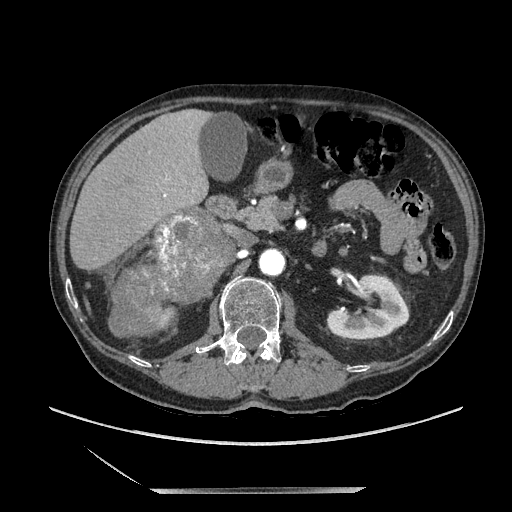
Contrast-enhanced abdominal CT, one axial slice. Soft-tissue window (W 400 / L 40 HU). 1.25 mm slice thickness. 512 × 512 image matrix, field of view 420 × 420 mm. Male patient. Case-level facts recorded for this patient, not image findings: diagnosis: adrenocortical carcinoma; tumour side: right adrenal; tumour size at pathology: 16 cm; Ki-67 index: 17 %; stage (as recorded): 3.
Outlined on this slice (semi-automatic segmentation, software-assisted and operator-edited):
- mass: bounding box <115,209,233,336> (left, top, right, bottom; pixels)